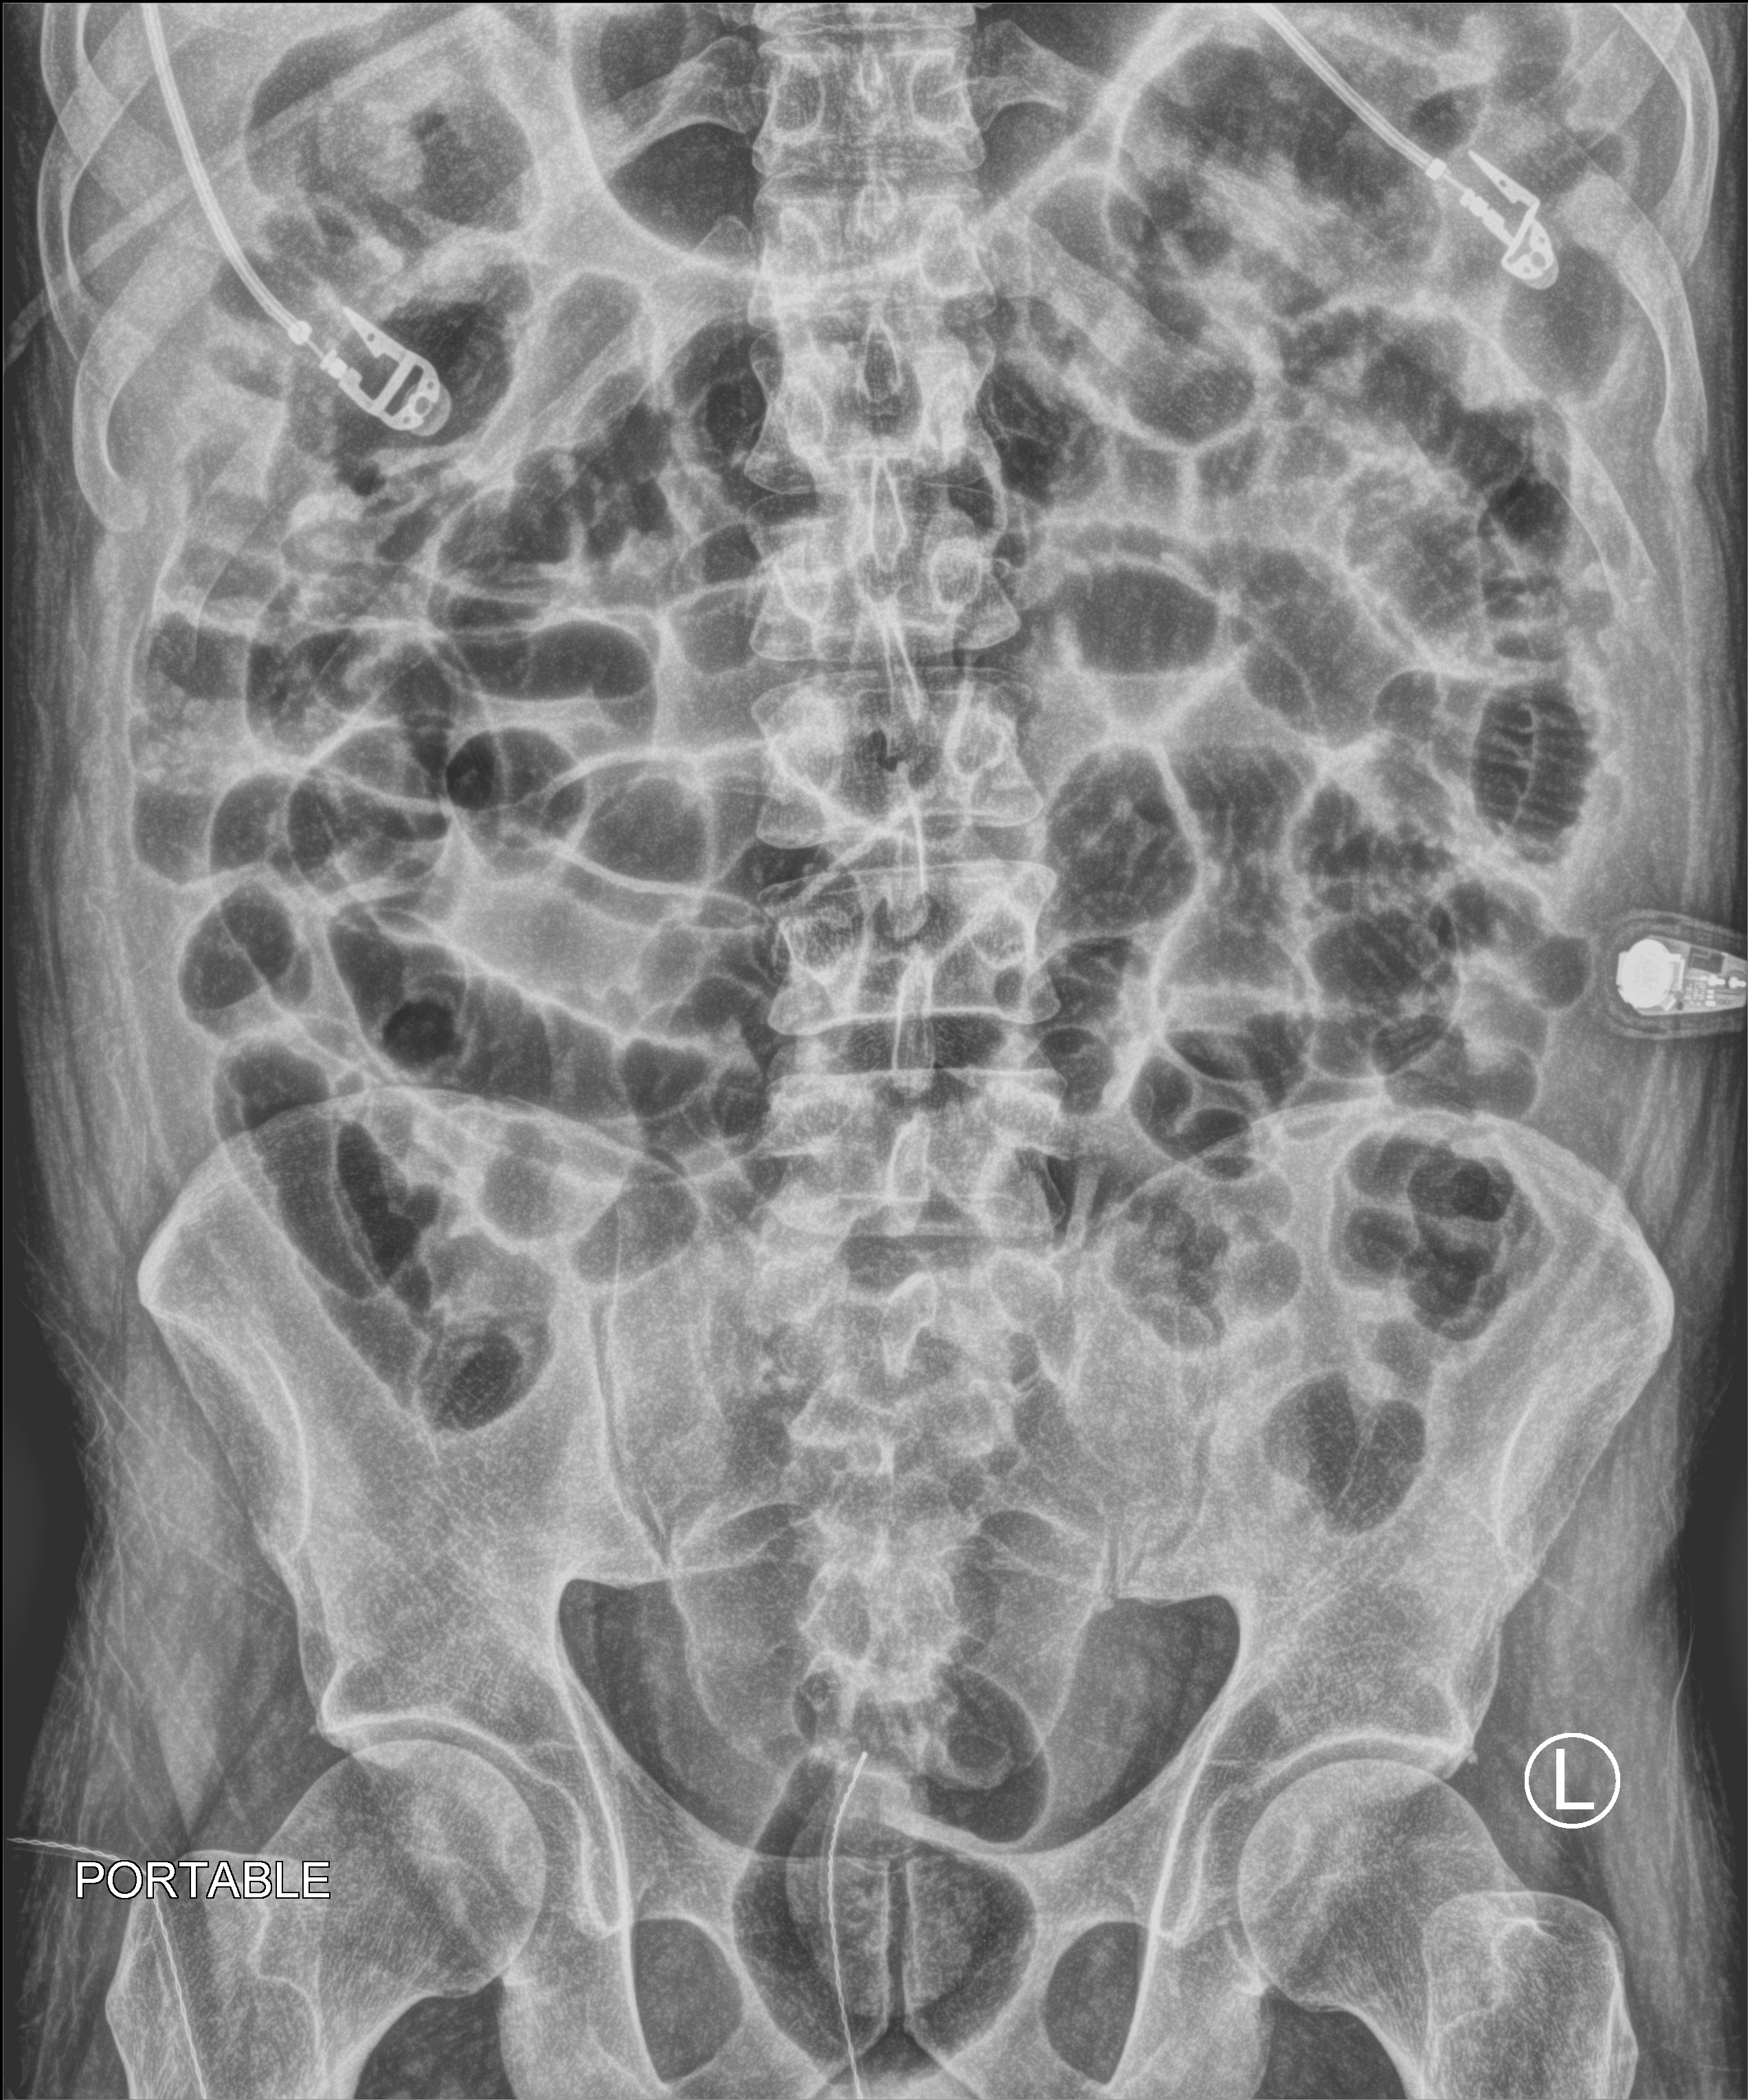
Portable abdomen radiograph. Male patient hospitalised with COVID-19, age 18–59 years.
From the hospital-stay record, not from the radiograph (when in the stay this image was taken is not recorded): mechanically ventilated during this hospital stay: yes; admitted to intensive care during this hospital stay: yes.